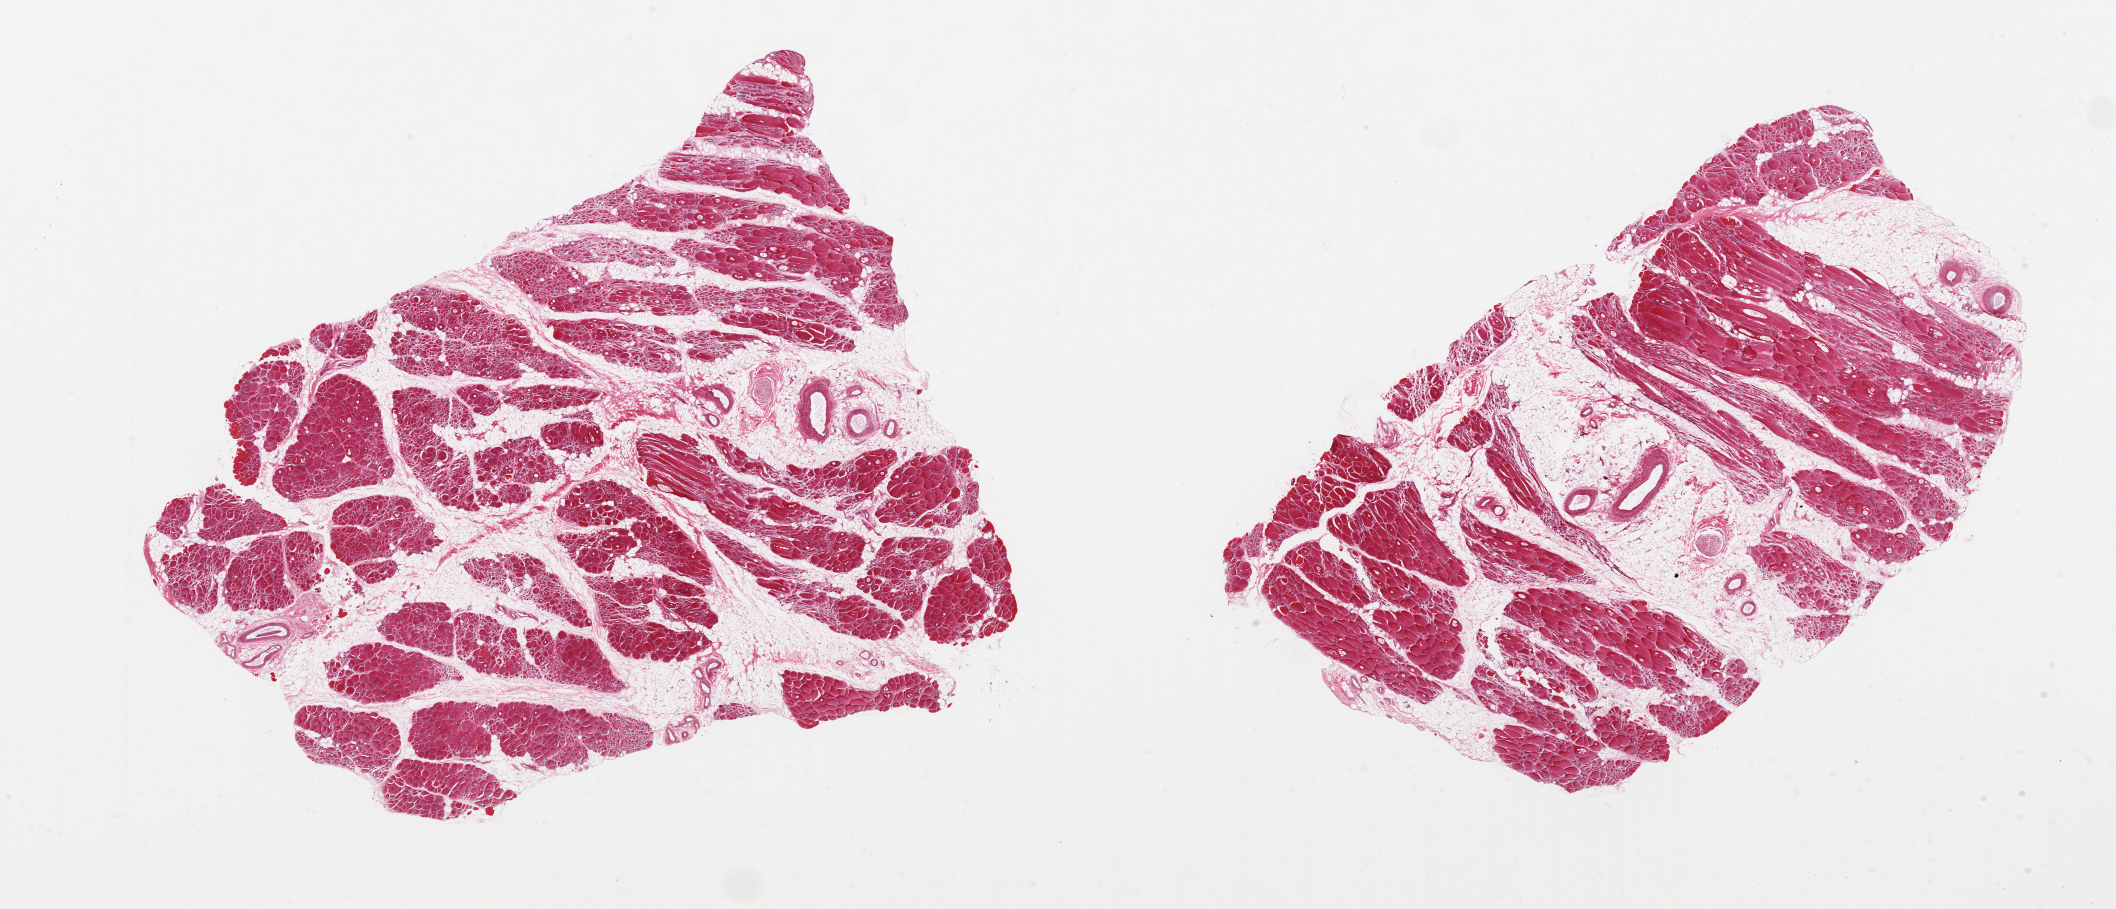
Digitized H&E-stained section — a low-resolution overview of the entire scanned area, about 33.5 x 14.4 mm, PAXgene-fixed, paraffin-embedded tissue, target tissue: skeletal muscle, tissue donor sample. Donor: male.
Review note (as recorded): 2 pieces. Moderate to severe atrophy. 20% and 40% internal fat.